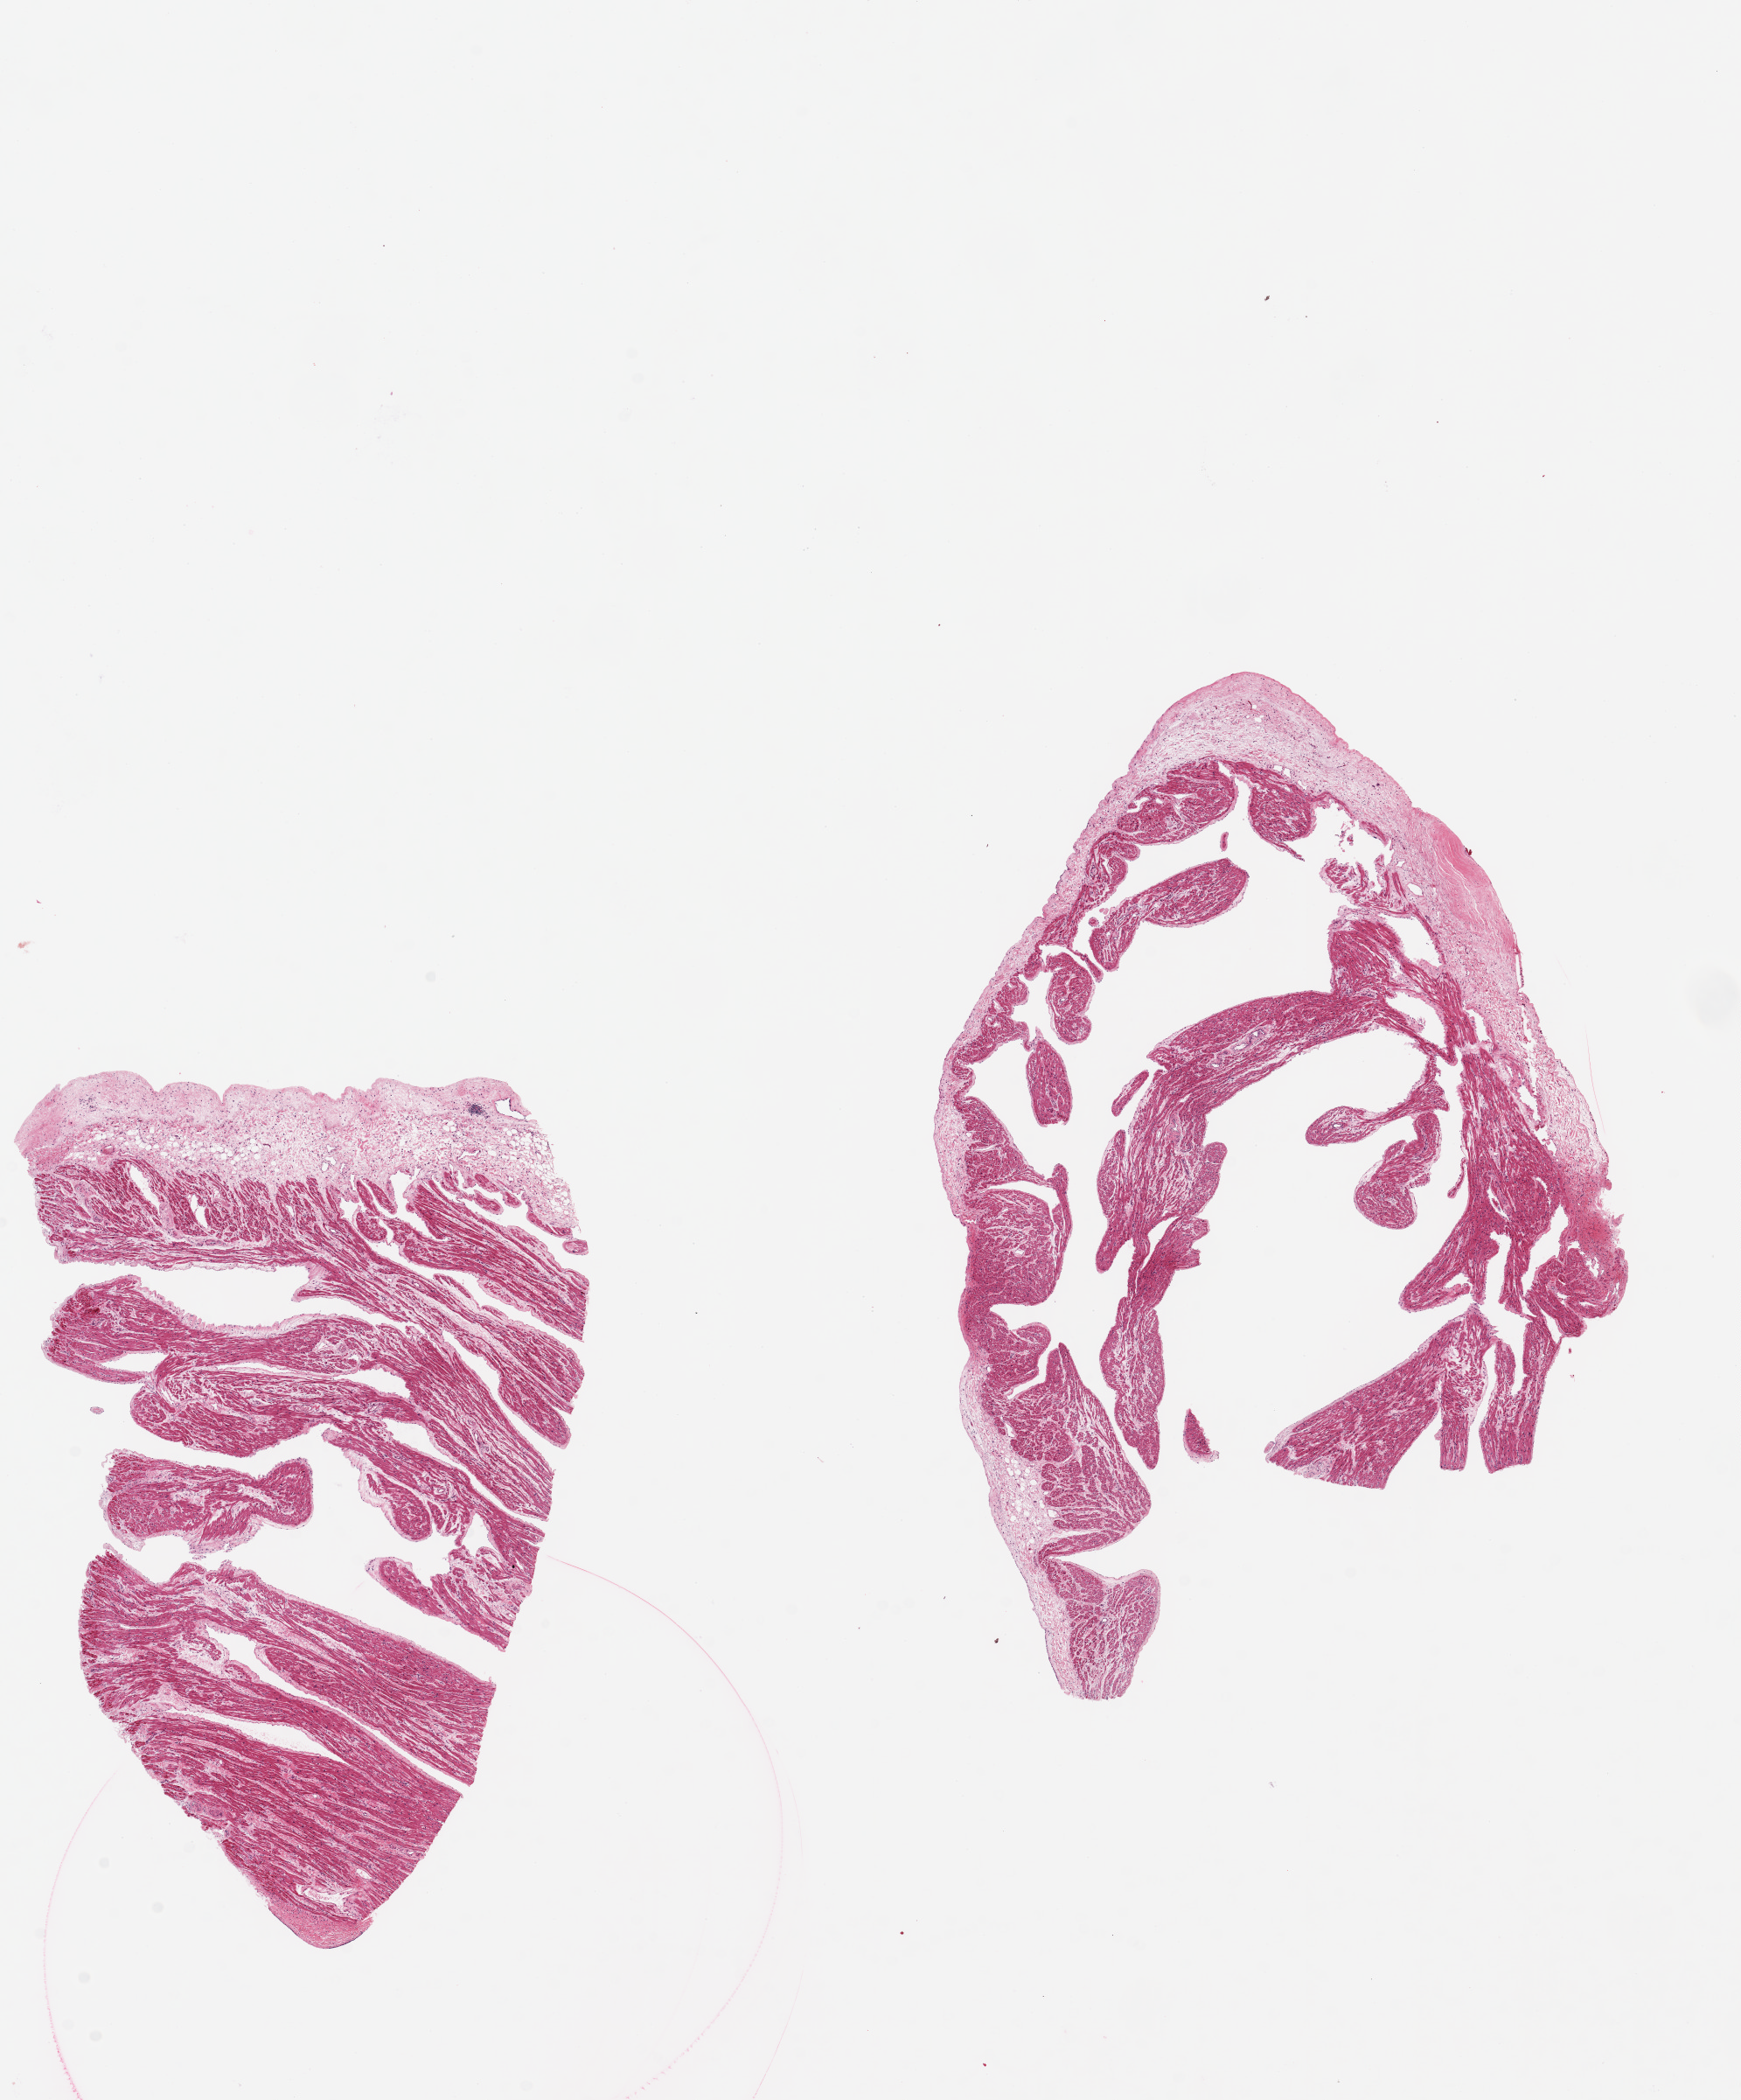
Hematoxylin and eosin (H&E) whole-slide image — whole scanned area (about 15.8 x 19.0 mm, from a 20x scan) shown as a low-resolution overview, PAXgene-fixed, paraffin-embedded tissue, section of auricular appendage (target tissue), donor tissue sample. Donor sex: male.
Pathologist's review note for this sample: 2 pieces, 9x6 & 8x5mm; preserved endothemium.